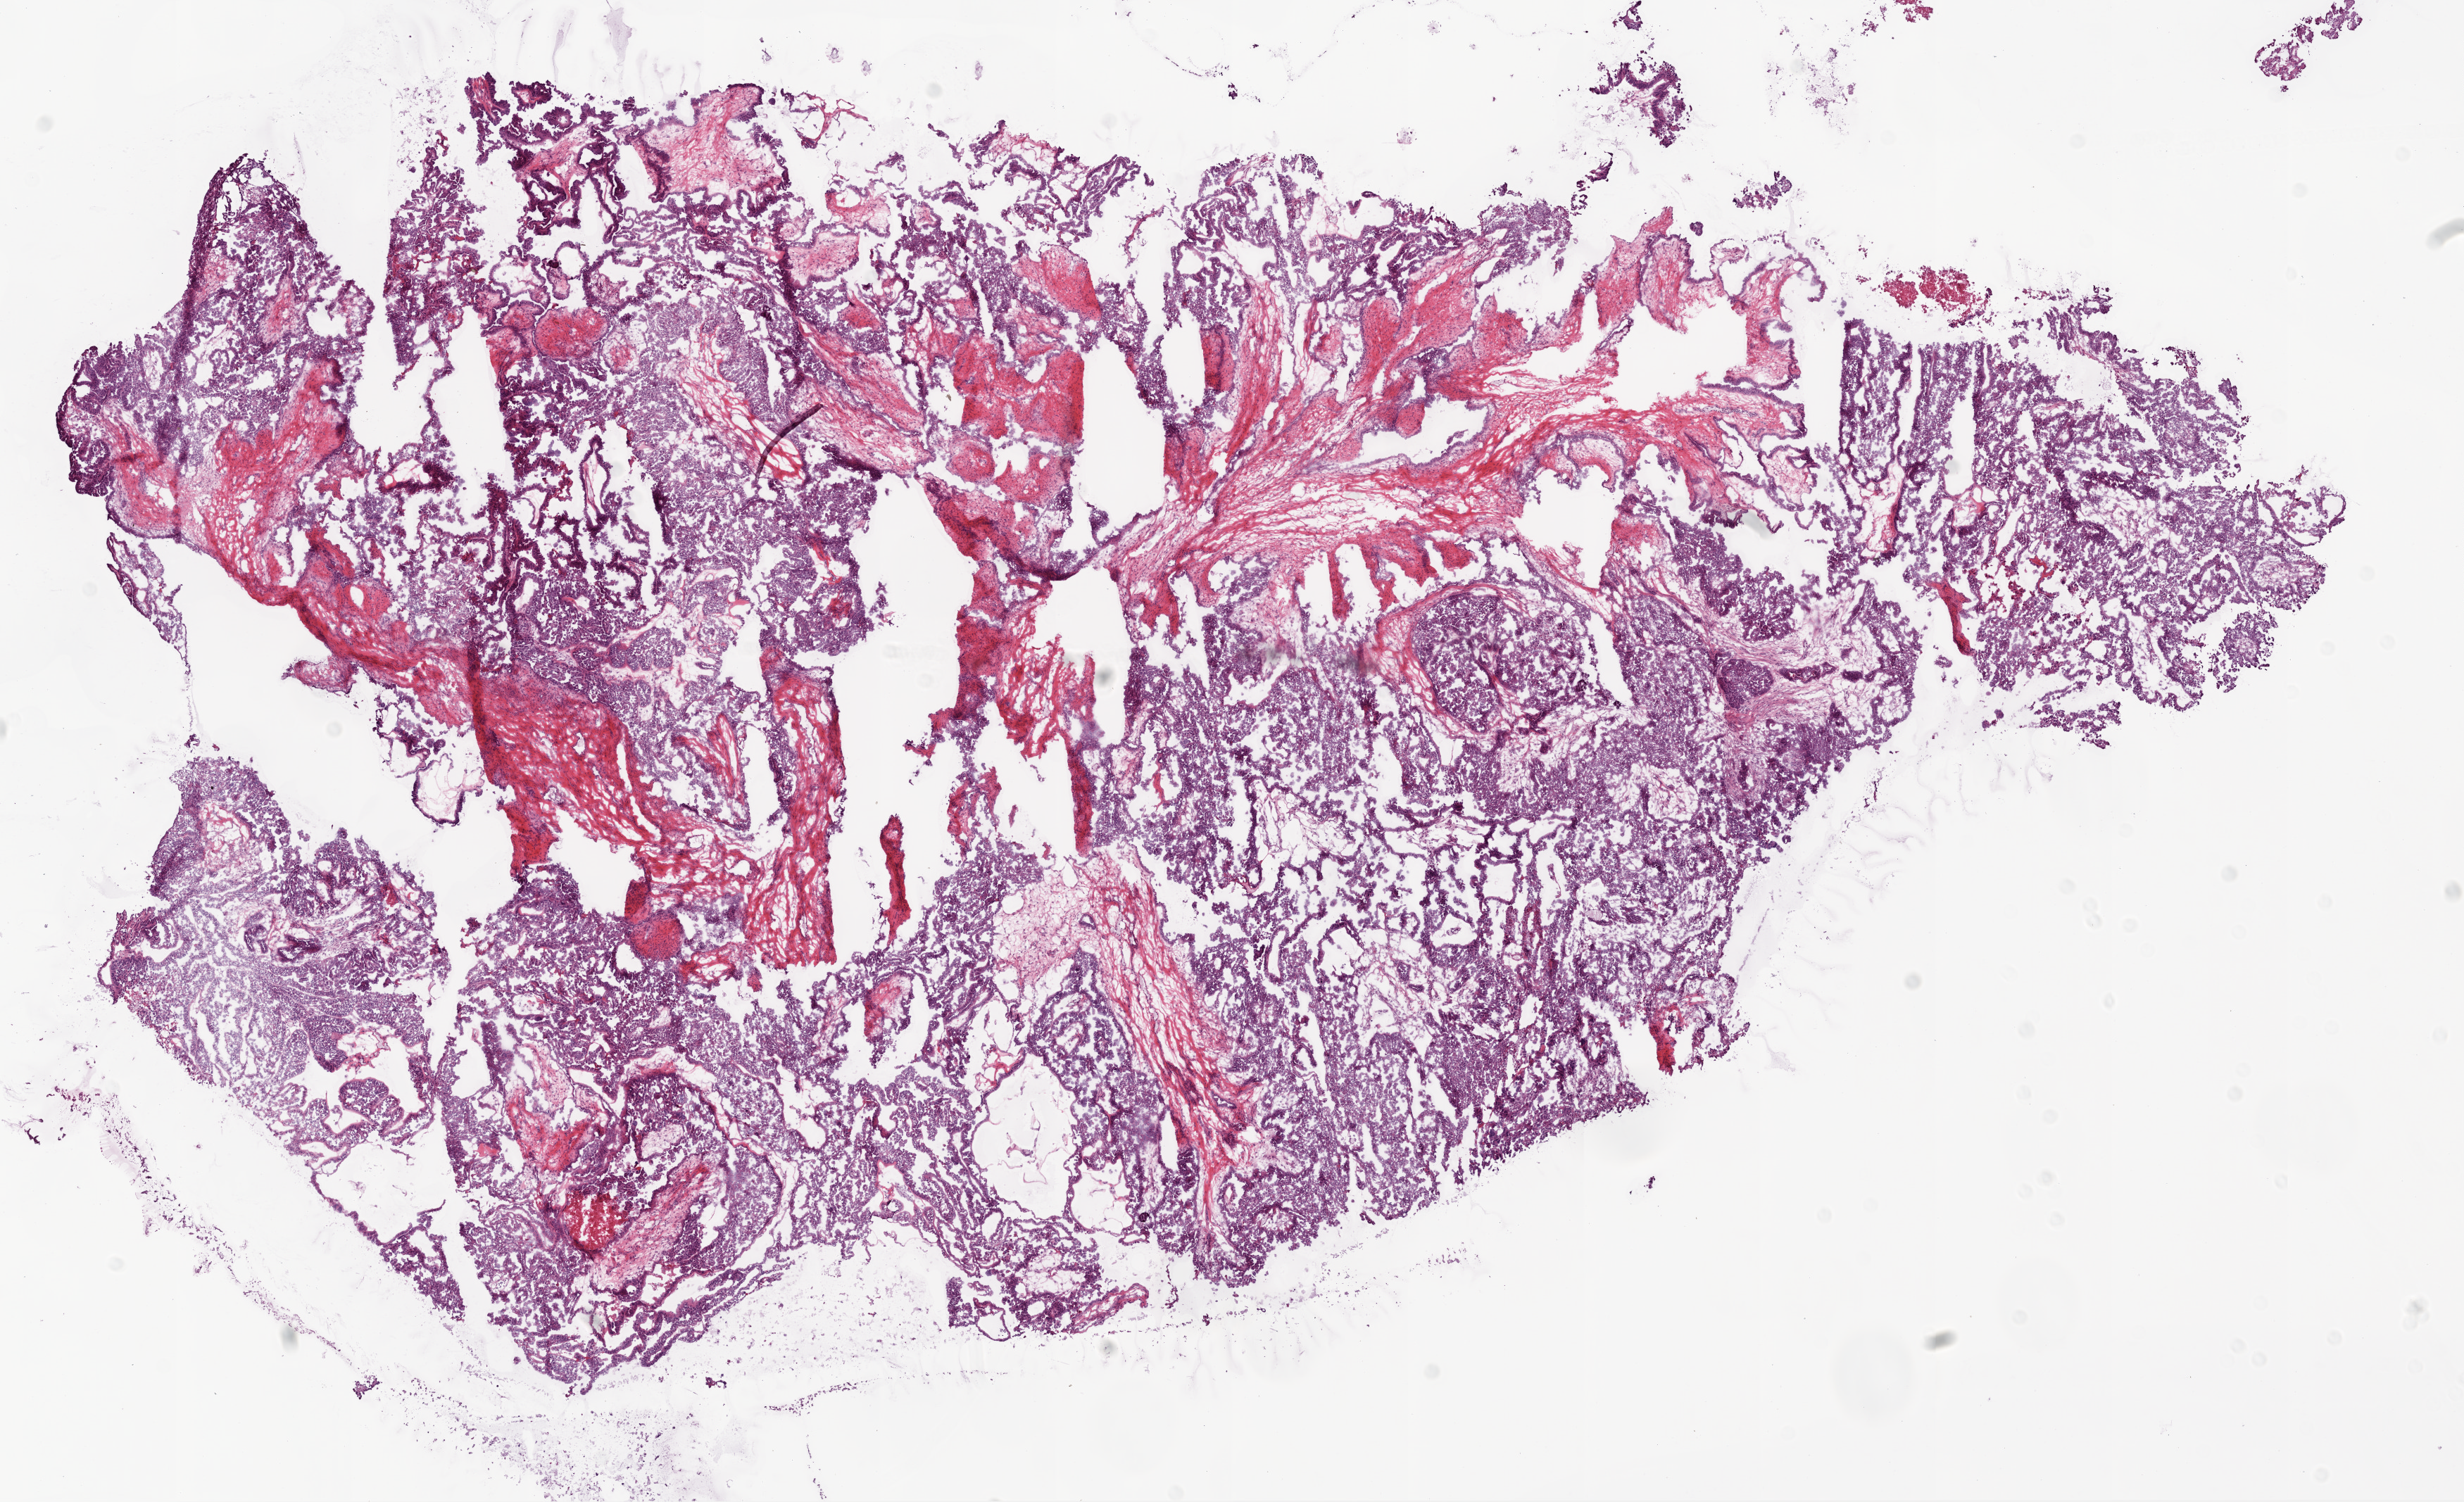
Whole-slide histology image, H&E — a low-resolution overview of the entire scanned area, about 14.0 x 8.6 mm; frozen section; primary tumour sample from the ovary. Female patient; age at initial diagnosis 59 years. Histologic grade: G3 (poorly differentiated). Composition of this section per pathologist review: tumour cells 85%, tumour nuclei 90%, normal cells 0%, stromal cells 0%, necrosis 15%.
Laterality: bilateral. FIGO stage: IV. Diagnosis: Serous cystadenocarcinoma, NOS.